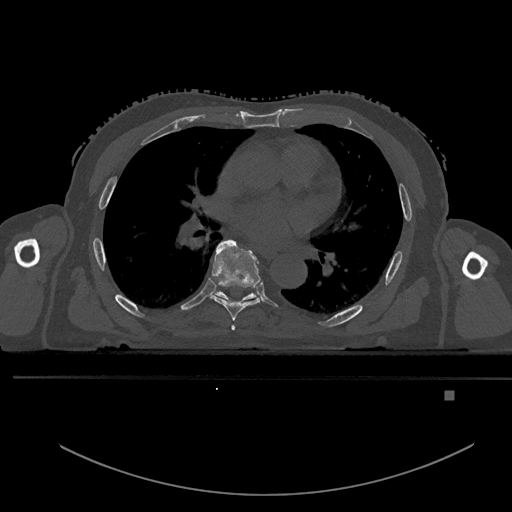
CT including the spine, one axial slice; position 290 of 969 along the scan axis; bone window (W 1800 / L 400 HU); 512 × 512 image matrix. Male patient, age 82 years. Case-level facts recorded for this patient, not image findings: primary cancer: prostate; vertebrae with lytic lesions (as recorded): T11, T9, T8, T2.
Annotated regions visible in this slice (semi-automatically segmented with operator editing):
- T5 vertebra: bounding box <231,325,236,331> (left, top, right, bottom; pixels)
- T6 vertebra: <209,239,261,321>
- T7 vertebra: <214,291,256,300>